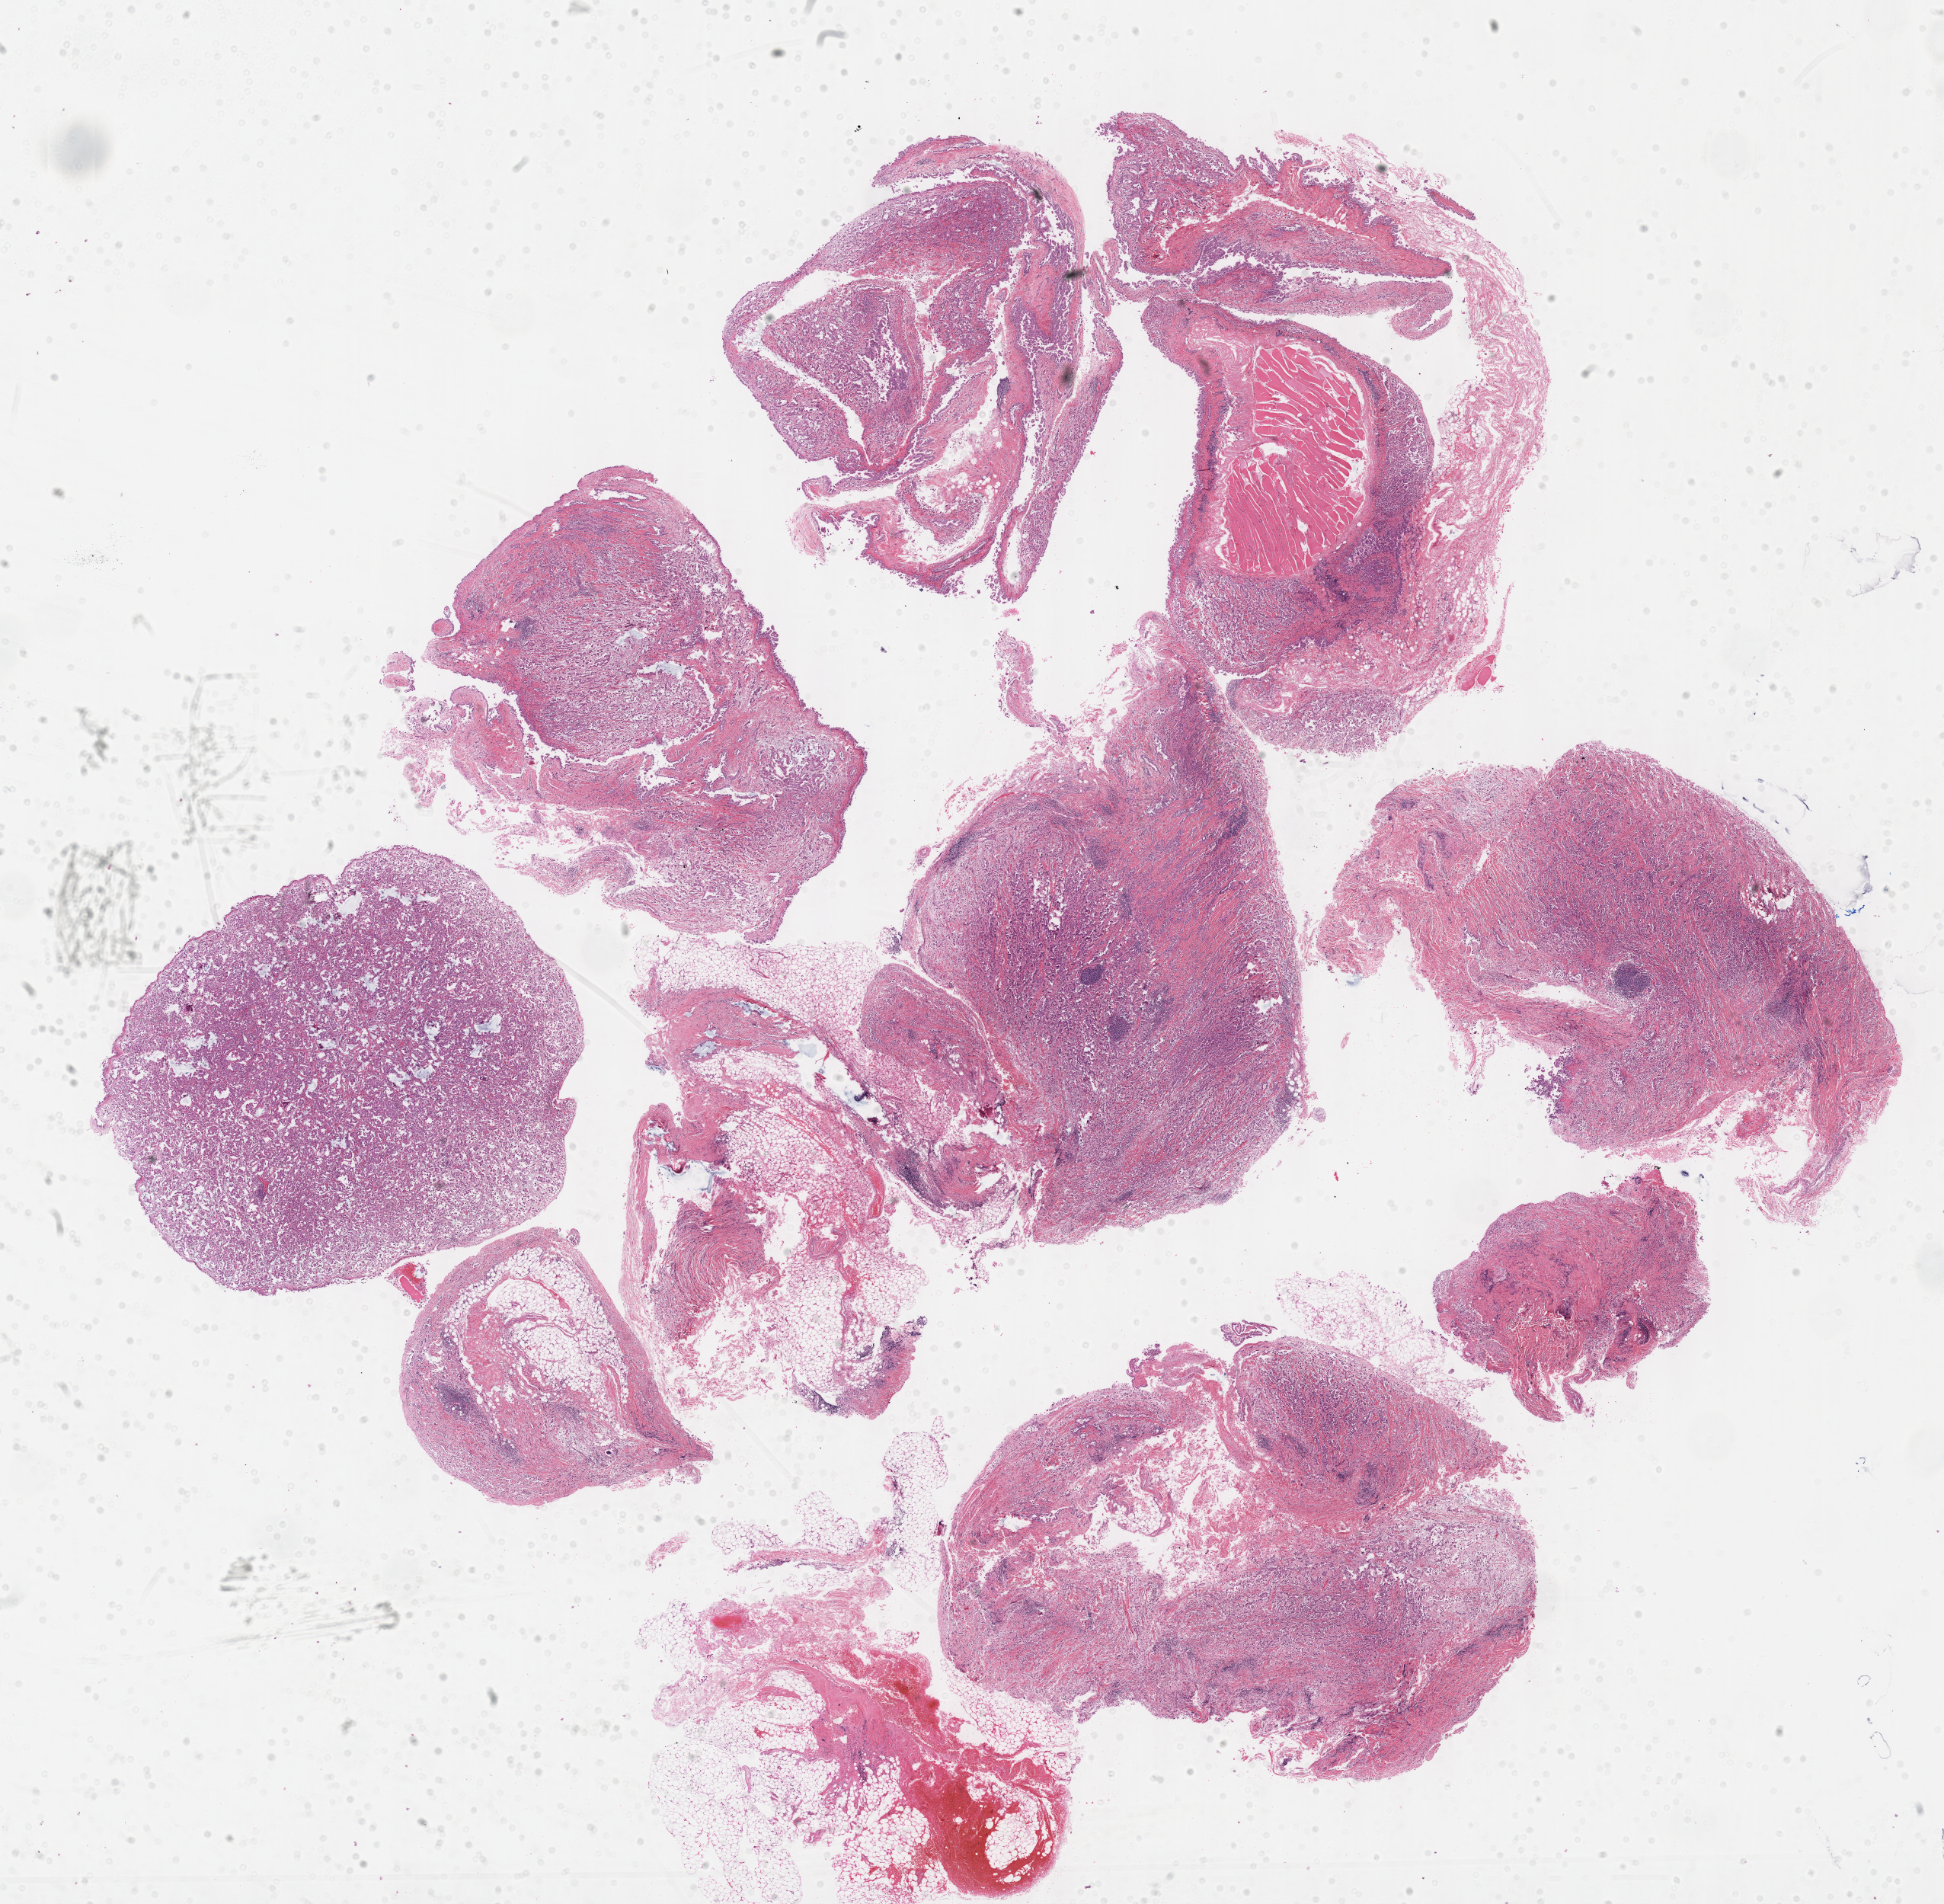
Whole-slide histology image, Hematoxylin and eosin (H&E) stained — low-resolution overview of the scanned area, about 20.6 x 20.2 mm (from a 40x scan). Formalin-fixed paraffin-embedded (FFPE) diagnostic section. Mesothelium, primary tumour sample. Patient: male, age at initial diagnosis 62 years.
Pathologic diagnosis: Epithelioid mesothelioma, malignant (pleura, NOS). AJCC pathologic stage: III.